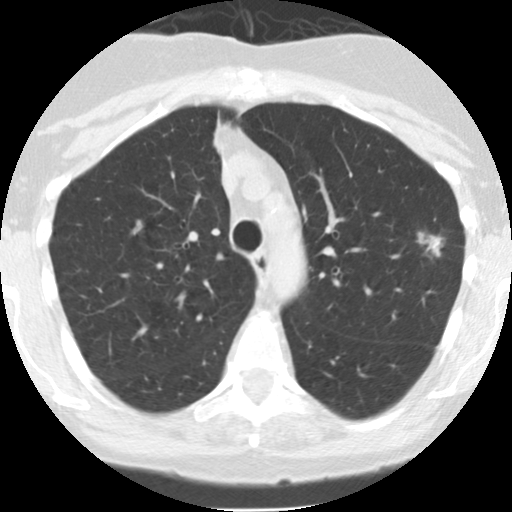
Low-dose screening chest CT, one axial slice; position 107 of 145 along the scan axis; 120 kVp; lung window (W 1500 / L -600 HU); 512 × 512 image matrix, field of view 280 × 280 mm.
Annotated regions visible in this slice (manually delineated by an expert):
- lesion 1 (tumor, upper lobe of left lung): bounding box [x1, y1, x2, y2] px = [417, 232, 444, 257]